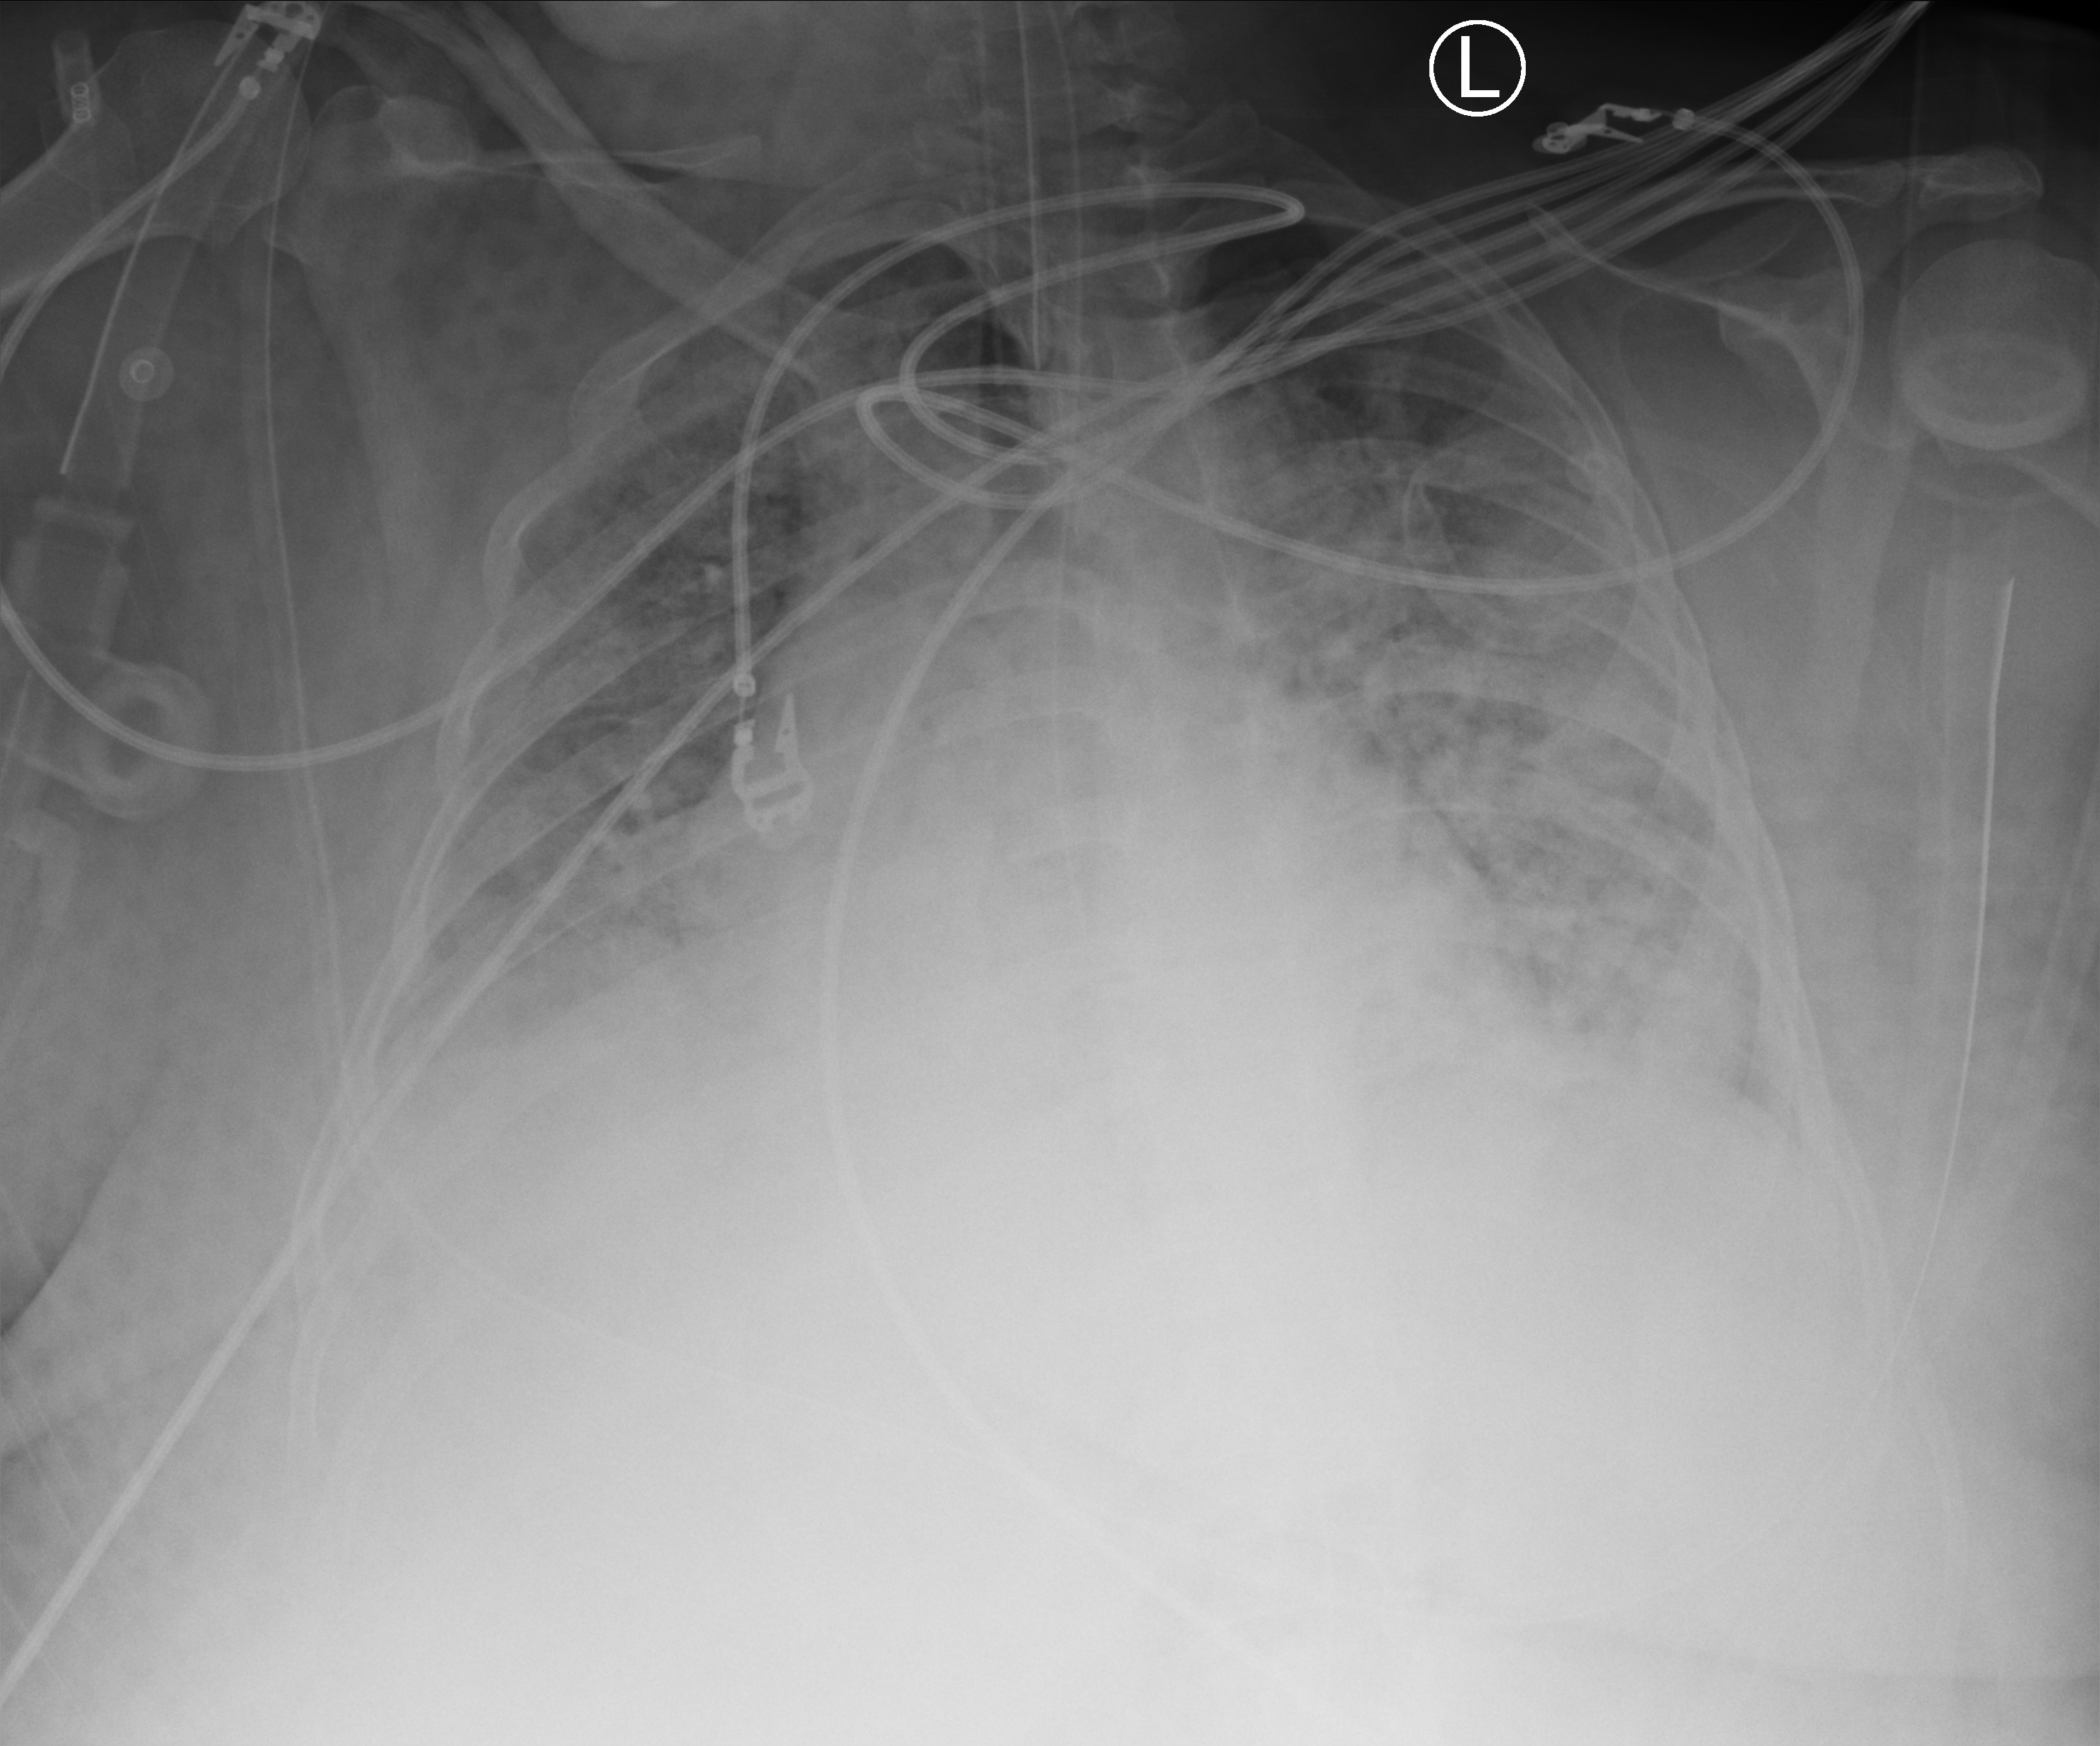
Portable chest radiograph, anteroposterior (AP) projection. Patient hospitalised with COVID-19; female, aged 18–59 years.
From the hospital-stay record, not from the radiograph (when in the stay this image was taken is not recorded):
- hypertension (admission record): no
- mechanically ventilated during this hospital stay: yes
- admitted to intensive care during this hospital stay: yes